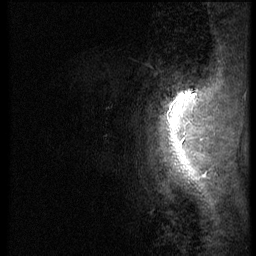
Breast MRI (dynamic contrast-enhanced), one sagittal slice. Slice 5 of 56 in the series (ordered by position). 3 images stored at this slice position (order not interpretable as contrast timing). 1.5 T. TE 4.2 ms, TR 9 ms. 2.5 mm slice thickness. 256 × 256 image matrix. Patient: female, 46 years. Case-level facts recorded for this patient, not image findings: setting: breast cancer imaged before/during neoadjuvant chemotherapy; receptor status: HER2-positive.
Outlined on this slice (semi-automatically segmented with operator editing):
- analysis volume of interest (the breast-tissue region the enhancement analysis was run in; not a lesion): bounding box <106,68,190,143> (left, top, right, bottom; pixels)
- tumour enhancement mask (voxels above the 140 % enhancement threshold inside the analysis volume of interest): <180,93,190,98>